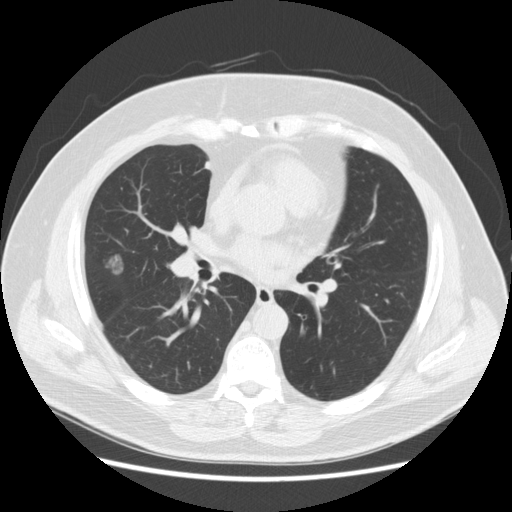
Axial slice from a low-dose chest CT screening exam, baseline annual screen, lung window (W 1500 / L -600 HU), 2.5 mm slice thickness, slice 109 of 213 in the series, 512 × 512 image matrix, field of view 380 × 380 mm. Male, age 67 years at enrolment.
Lesion marked by an expert reader, bounding box [x1, y1, x2, y2] px = [93, 250, 130, 285]. The exam's reader record, not a measurement of the box and not confirmed to be the same lesion: non-calcified nodule or mass ≥4 mm, right middle lobe, 15 × 11 mm, smooth margins, soft tissue attenuation. Participant outcome: lung cancer diagnosed 409 days after this screen (after the second annual screen) — adenocarcinoma, NOS, right middle lobe, moderately differentiated (G2), stage IA (AJCC 6th edition), 14 mm at pathology.